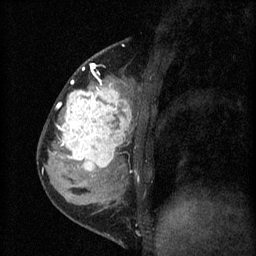
Breast MRI (dynamic contrast-enhanced), one sagittal slice; slice 21 of 60 in the series (ordered by position); 3 images stored at this slice position (order not interpretable as contrast timing); 1.5 T; TE 4.2 ms, TR 8.2 ms; 2 mm slice thickness; 256 × 256 image matrix, field of view 180 × 180 mm. Patient: female, 37 years.
Structures marked on this image (semi-automatic segmentation, software-assisted and operator-edited):
- analysis volume of interest (the breast-tissue region the enhancement analysis was run in; not a lesion): bounding box (x1, y1, x2, y2) in pixels: (53, 78, 140, 181)
- tumour enhancement mask (voxels above the 70 % enhancement threshold inside the analysis volume of interest): (55, 80, 132, 171)